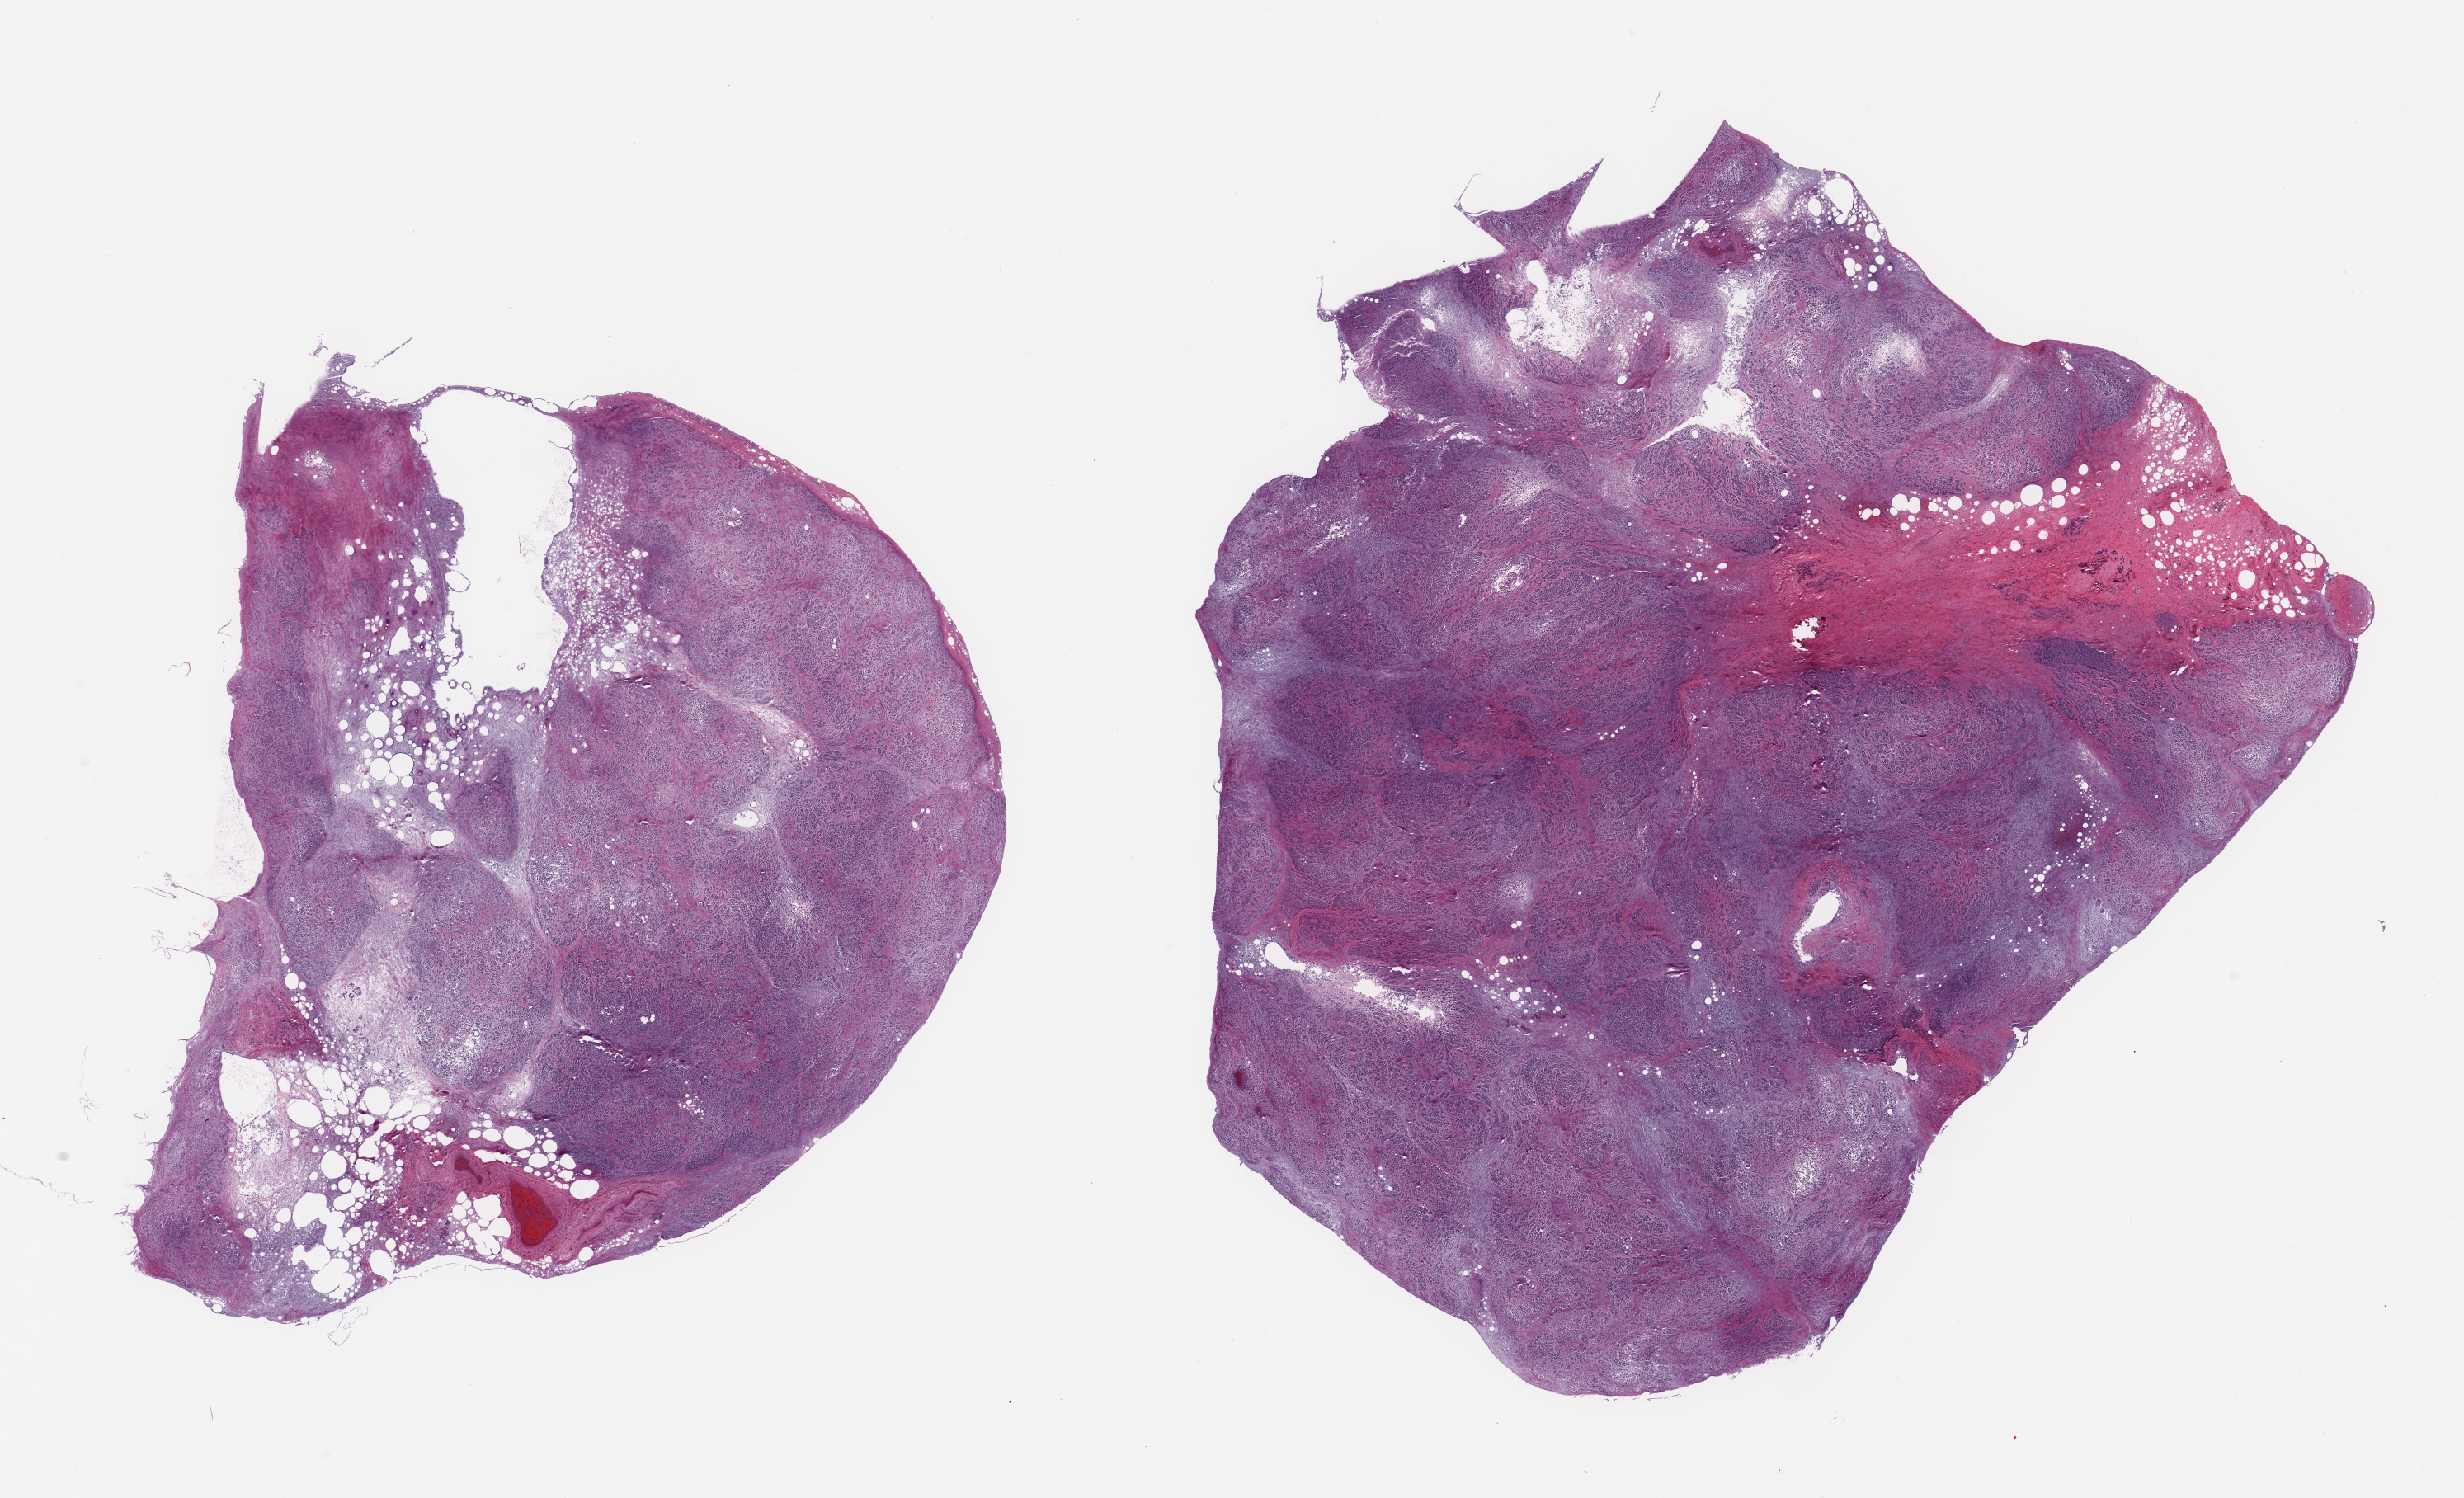
Whole-slide image, H&E stain, shown as a low-resolution overview of the whole scanned area (about 23.6 x 14.4 mm). PAXgene-fixed, paraffin-embedded tissue. Target tissue: pancreas. Tissue donor sample. Donor sex: male.
Reviewer comment on this tissue sample: 2 pieces, advanced saponification; islets not visible.